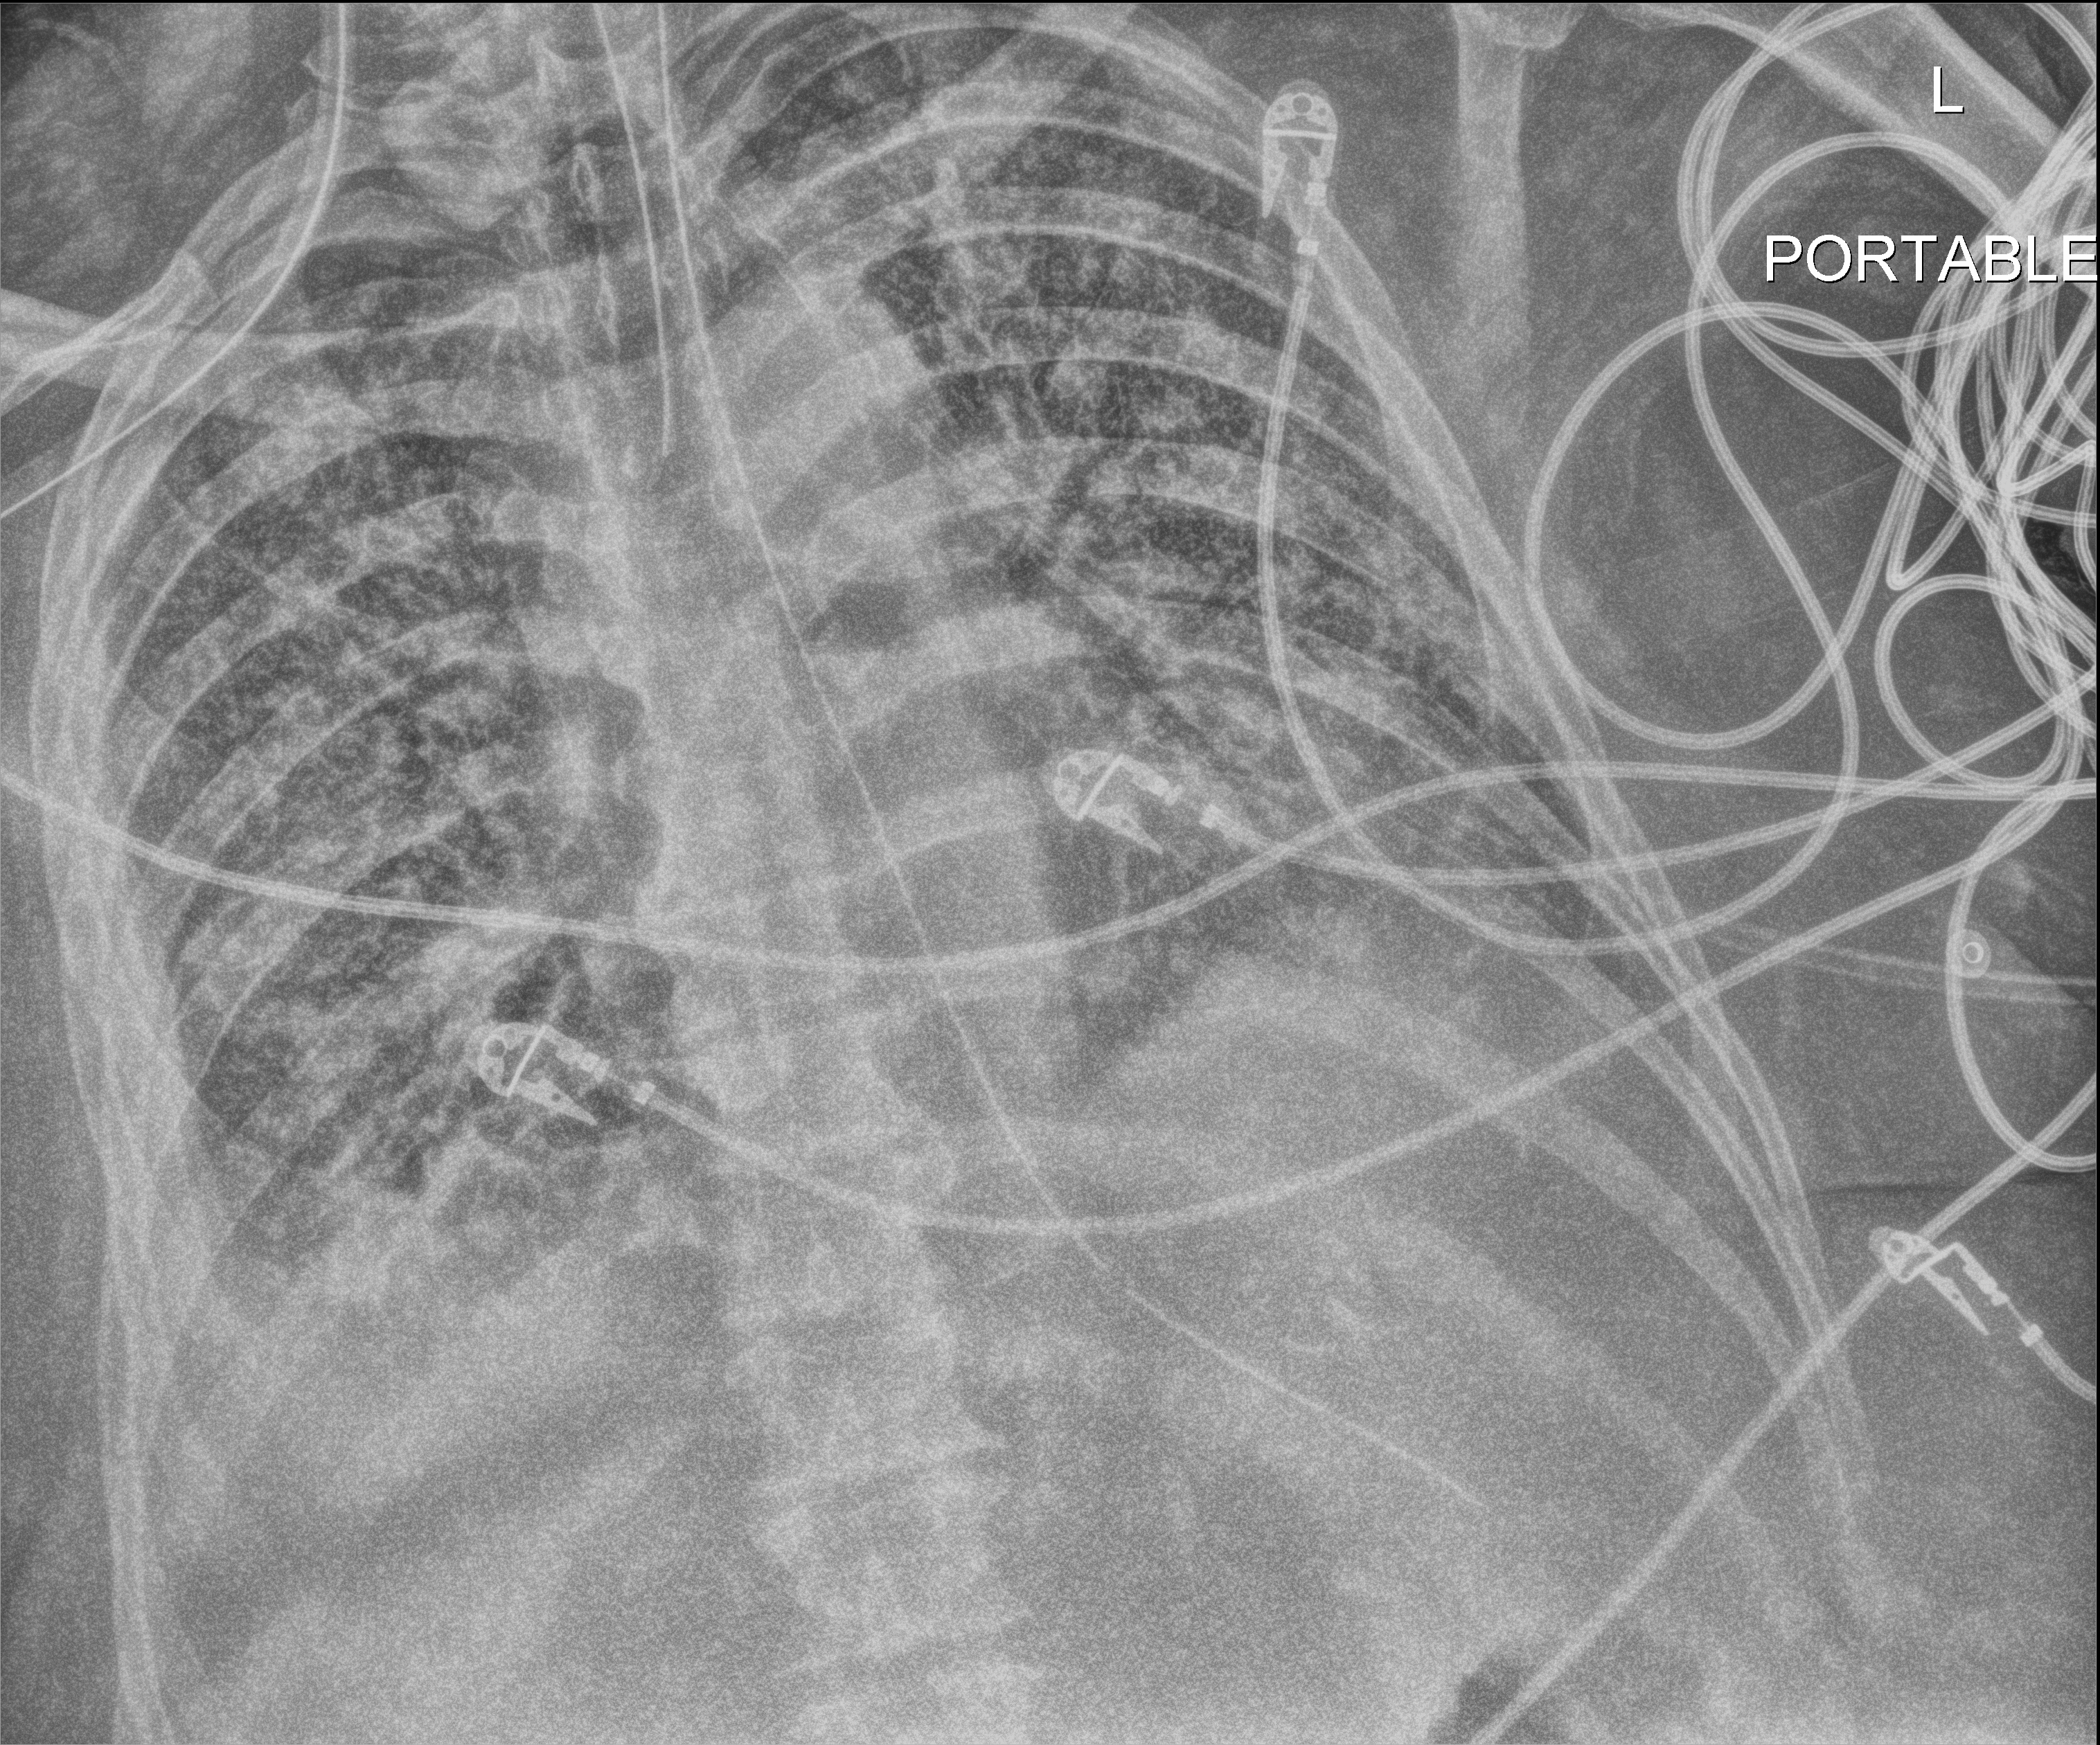
Bedside chest radiograph (digital radiography), anteroposterior (AP) projection. Male patient hospitalised with COVID-19, age 60–74 years.
From the hospital-stay record, not from the radiograph (when in the stay this image was taken is not recorded): diabetes (admission record): no.